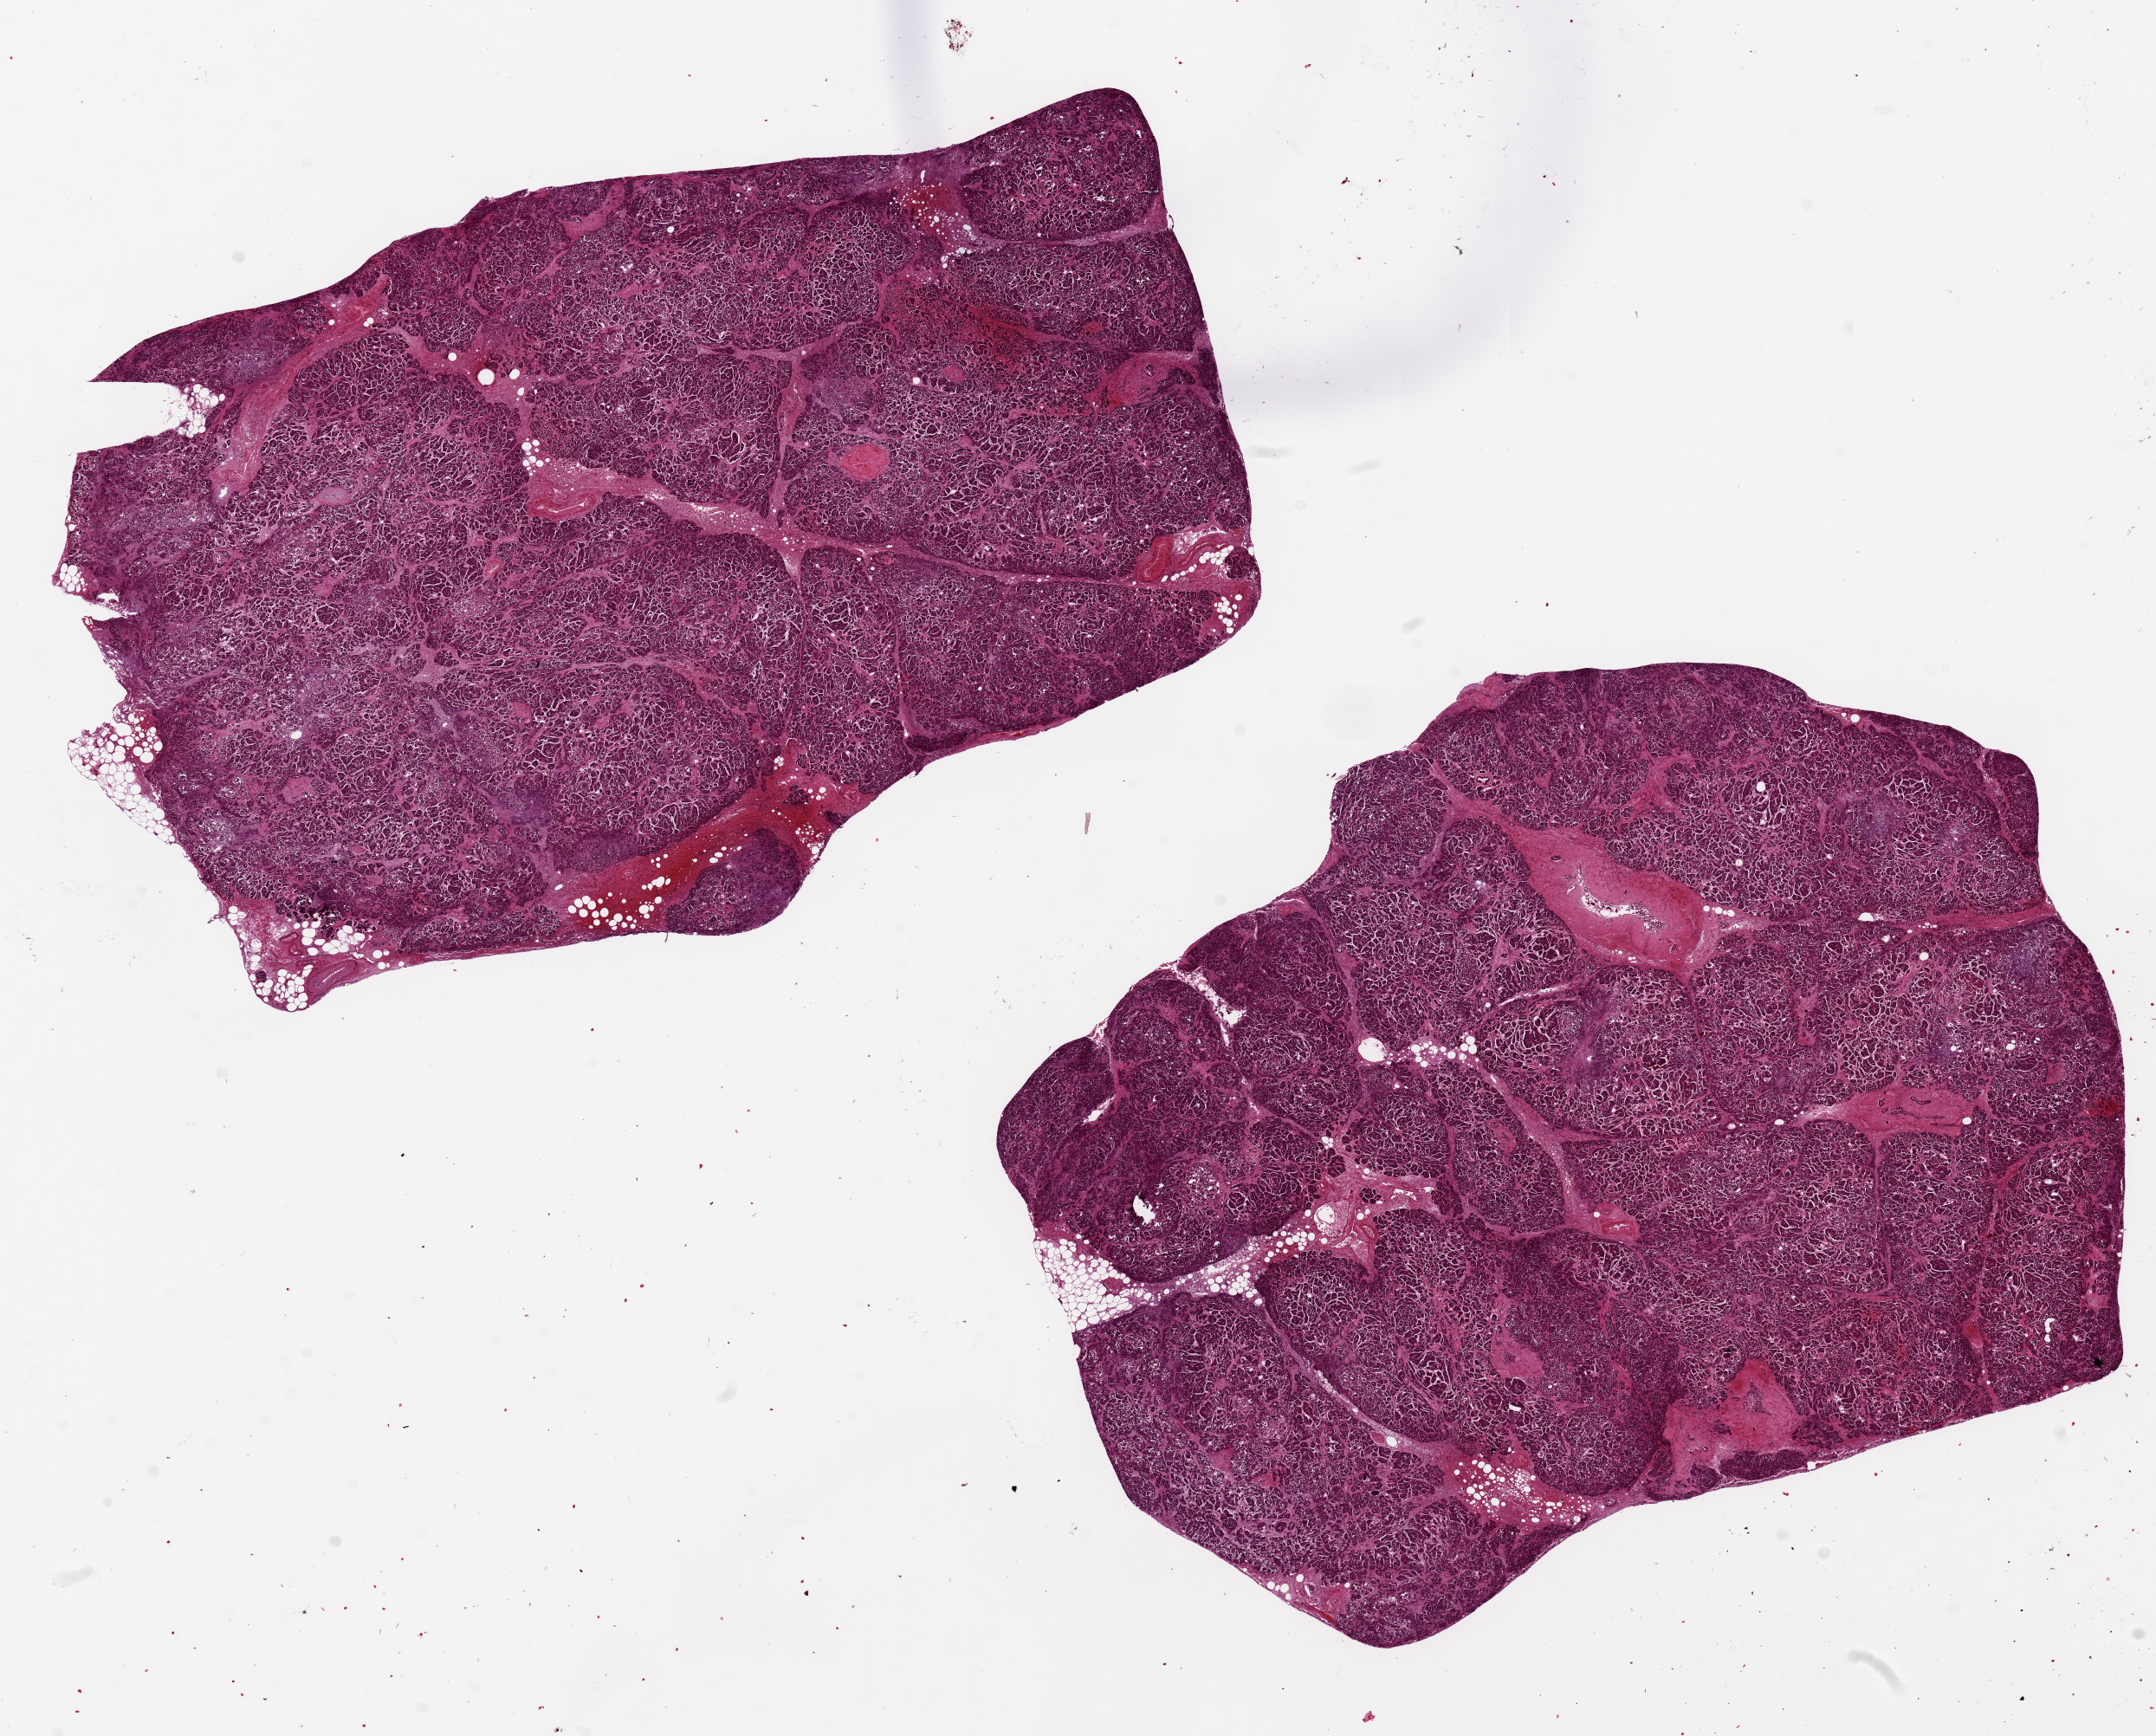
Digitized H&E-stained section, whole scanned area (about 19.7 x 15.9 mm) shown as a low-resolution overview, PAXgene-fixed, paraffin-embedded tissue, target tissue: pancreas, donor tissue sample. Donor: male.
- pathologist's review note for this sample: 2 pieces ~10x6mm, minimal adherent fat, saponification, Islets not well seen